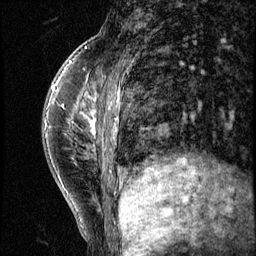
Breast MRI (dynamic contrast-enhanced), one sagittal slice. Slice 18 of 56 in the series (ordered by position). 3 images stored at this slice position (order not interpretable as contrast timing). 1.5 T. TE 4.2 ms, TR 8.7 ms. 2.5 mm slice thickness. 256 × 256 image matrix, field of view 180 × 180 mm. Female patient, age 35 years. Case-level facts recorded for this patient, not image findings: setting: breast cancer imaged before/during neoadjuvant chemotherapy; receptor status: HER2-positive.
Structures marked on this image (semi-automatically segmented with operator editing):
- analysis volume of interest (the breast-tissue region the enhancement analysis was run in; not a lesion): bounding box <58,84,138,186> (left, top, right, bottom; pixels)
- tumour enhancement mask (voxels above the 140 % enhancement threshold inside the analysis volume of interest): <91,93,118,171>